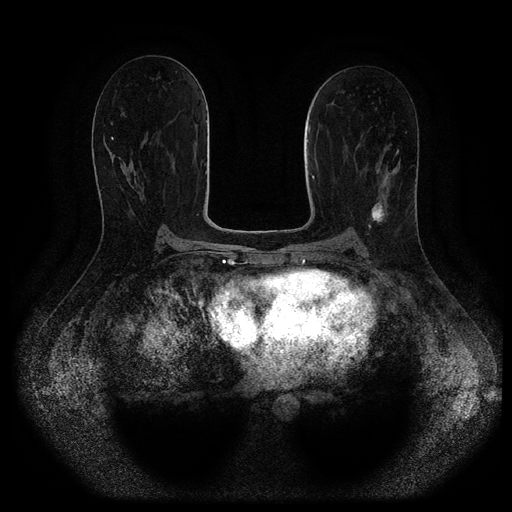
Breast MRI (dynamic contrast-enhanced, multi-phase), one axial slice. Position 56 of 116 along the scan axis. Dynamic contrast-enhanced series, time point 2 of 5 at this slice position (early post-contrast). 1.5 T. TE 2.6 ms, TR 5.3 ms. 2 mm slice thickness. 512 × 512 image matrix. Patient: female, 45 years.
Outlined on this slice (semi-automatically segmented with operator editing):
- breast lesion (labelled 'tumour' in the annotation; benign lesions carry a separate 'benign' label): bounding box [x1, y1, x2, y2] px = [369, 198, 388, 225]